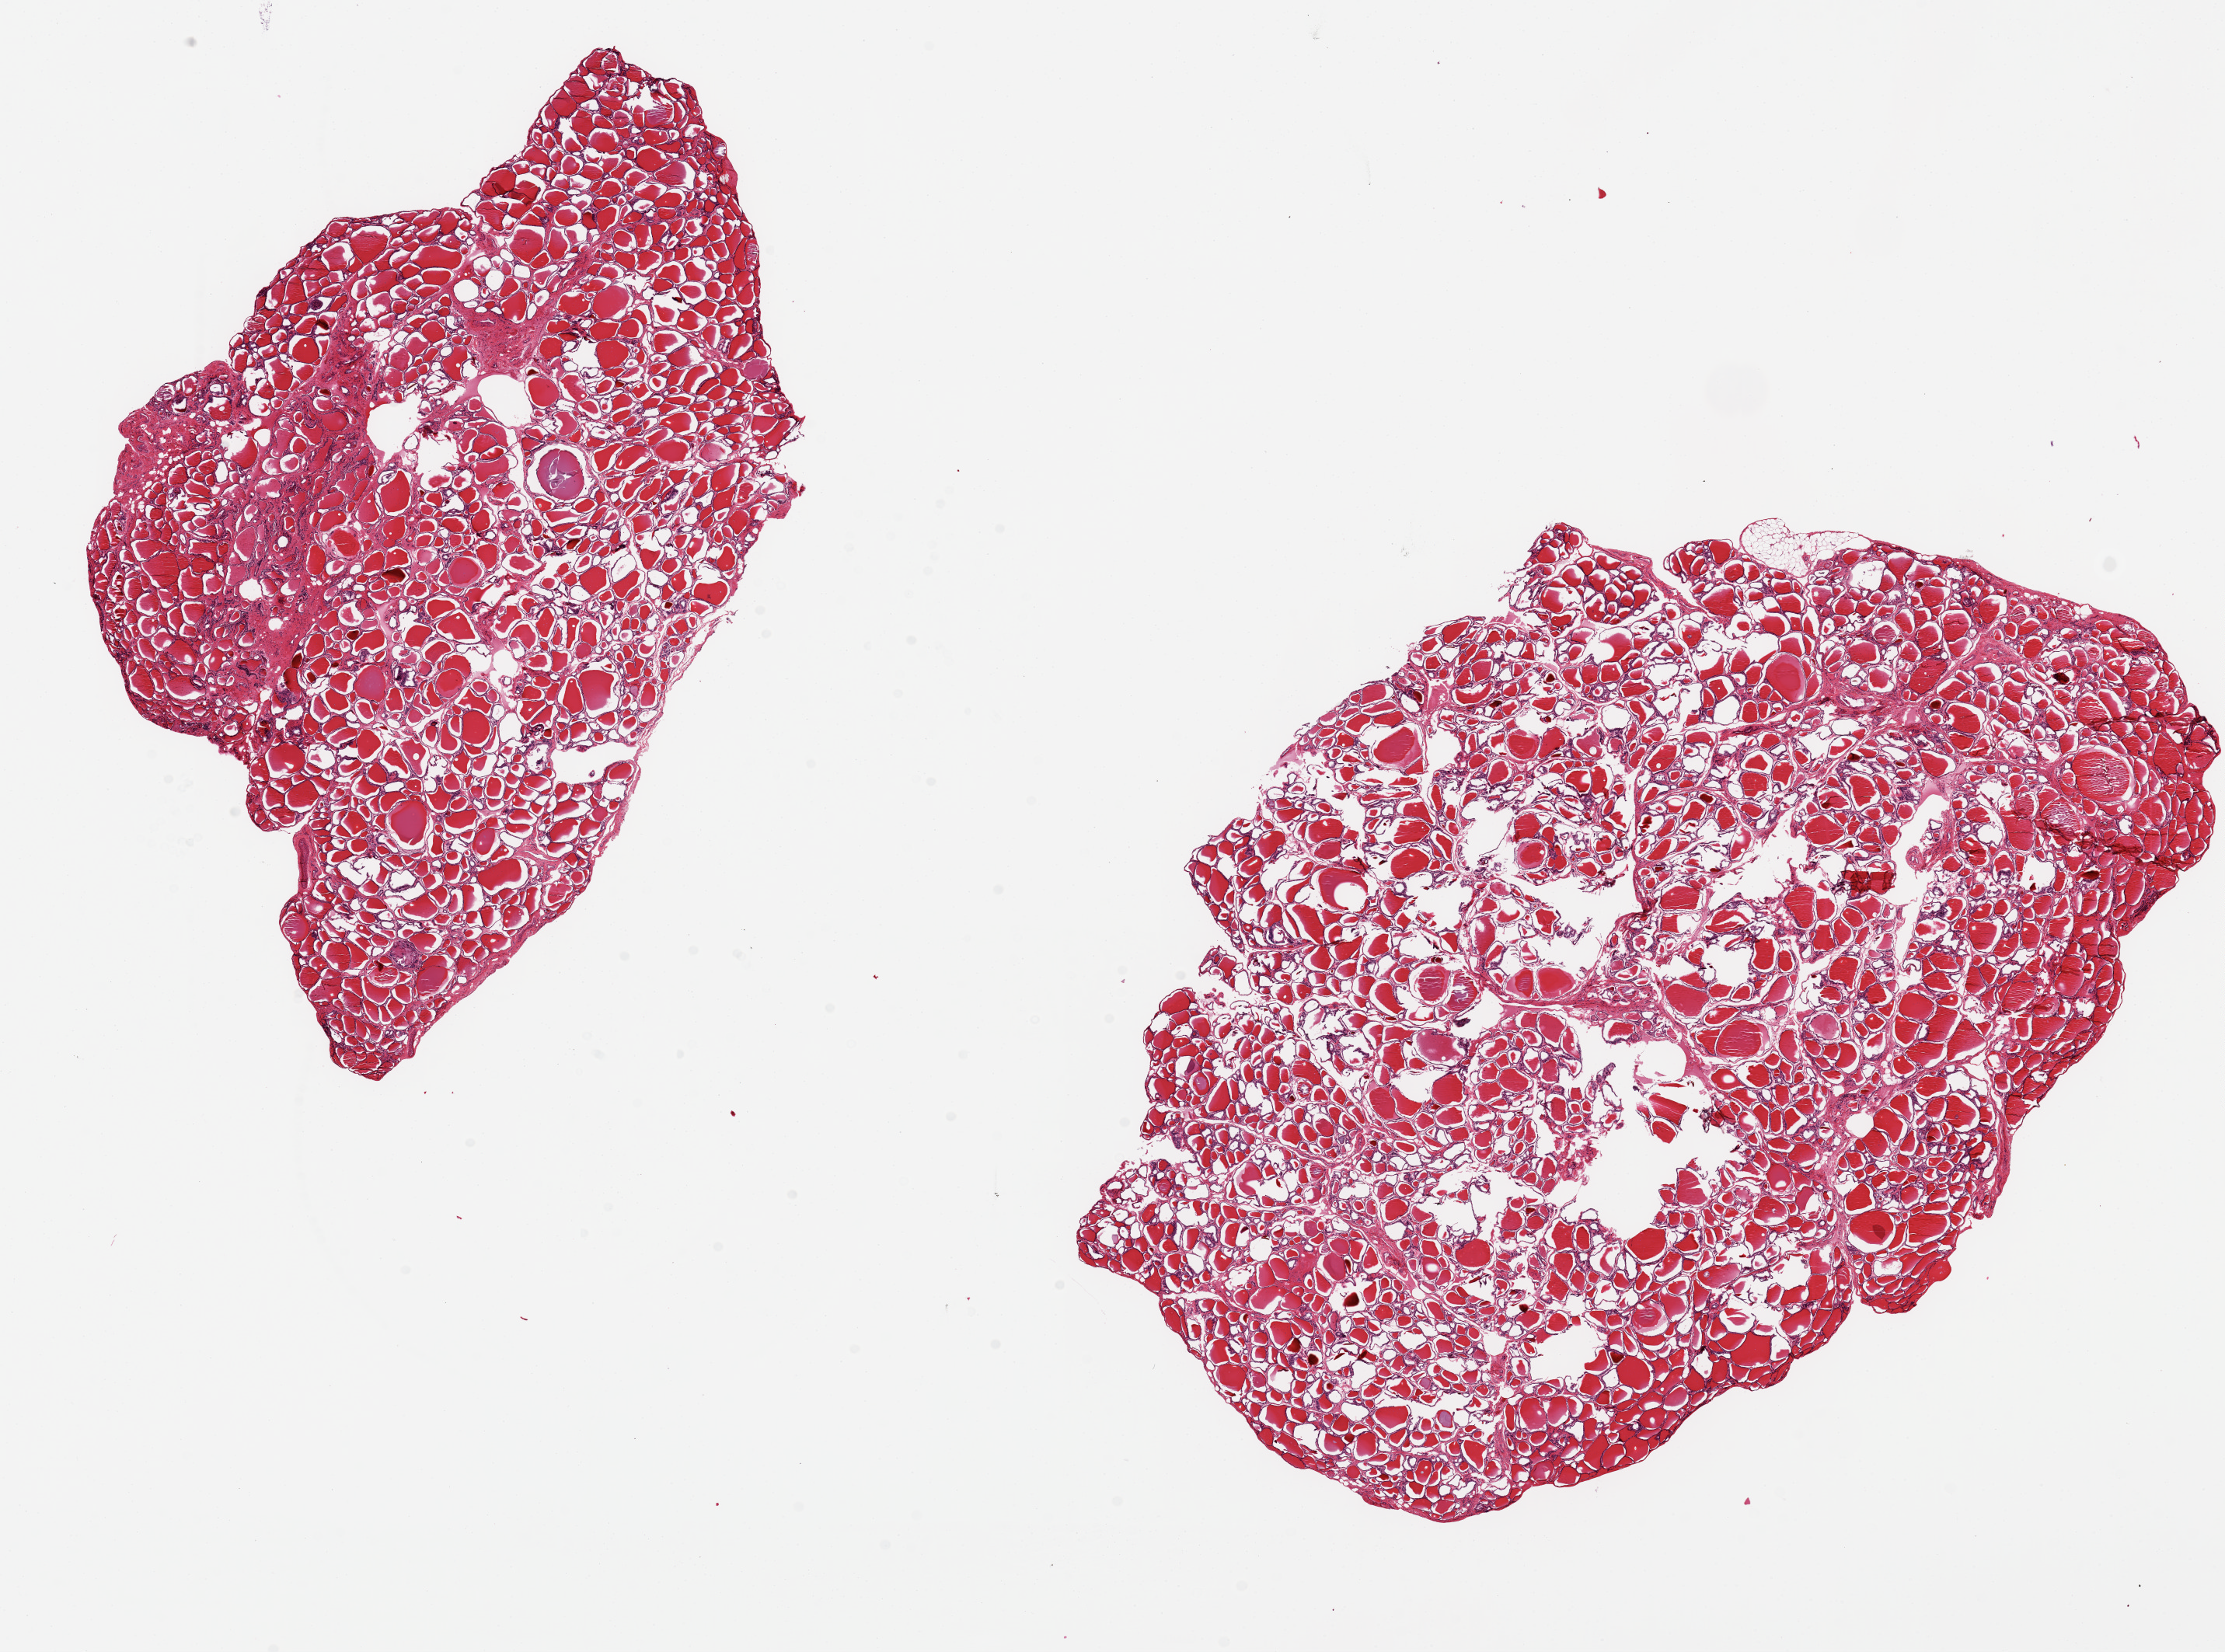
Hematoxylin and eosin (H&E) whole-slide image, brightfield, low-resolution overview of the scanned area, about 22.6 x 16.8 mm (from a 20x scan), PAXgene-fixed paraffin-embedded (PFPE) section, section of thyroid (target tissue), donor tissue sample.
Reviewer comment on this tissue sample: 2 ~11x7mm pieces.